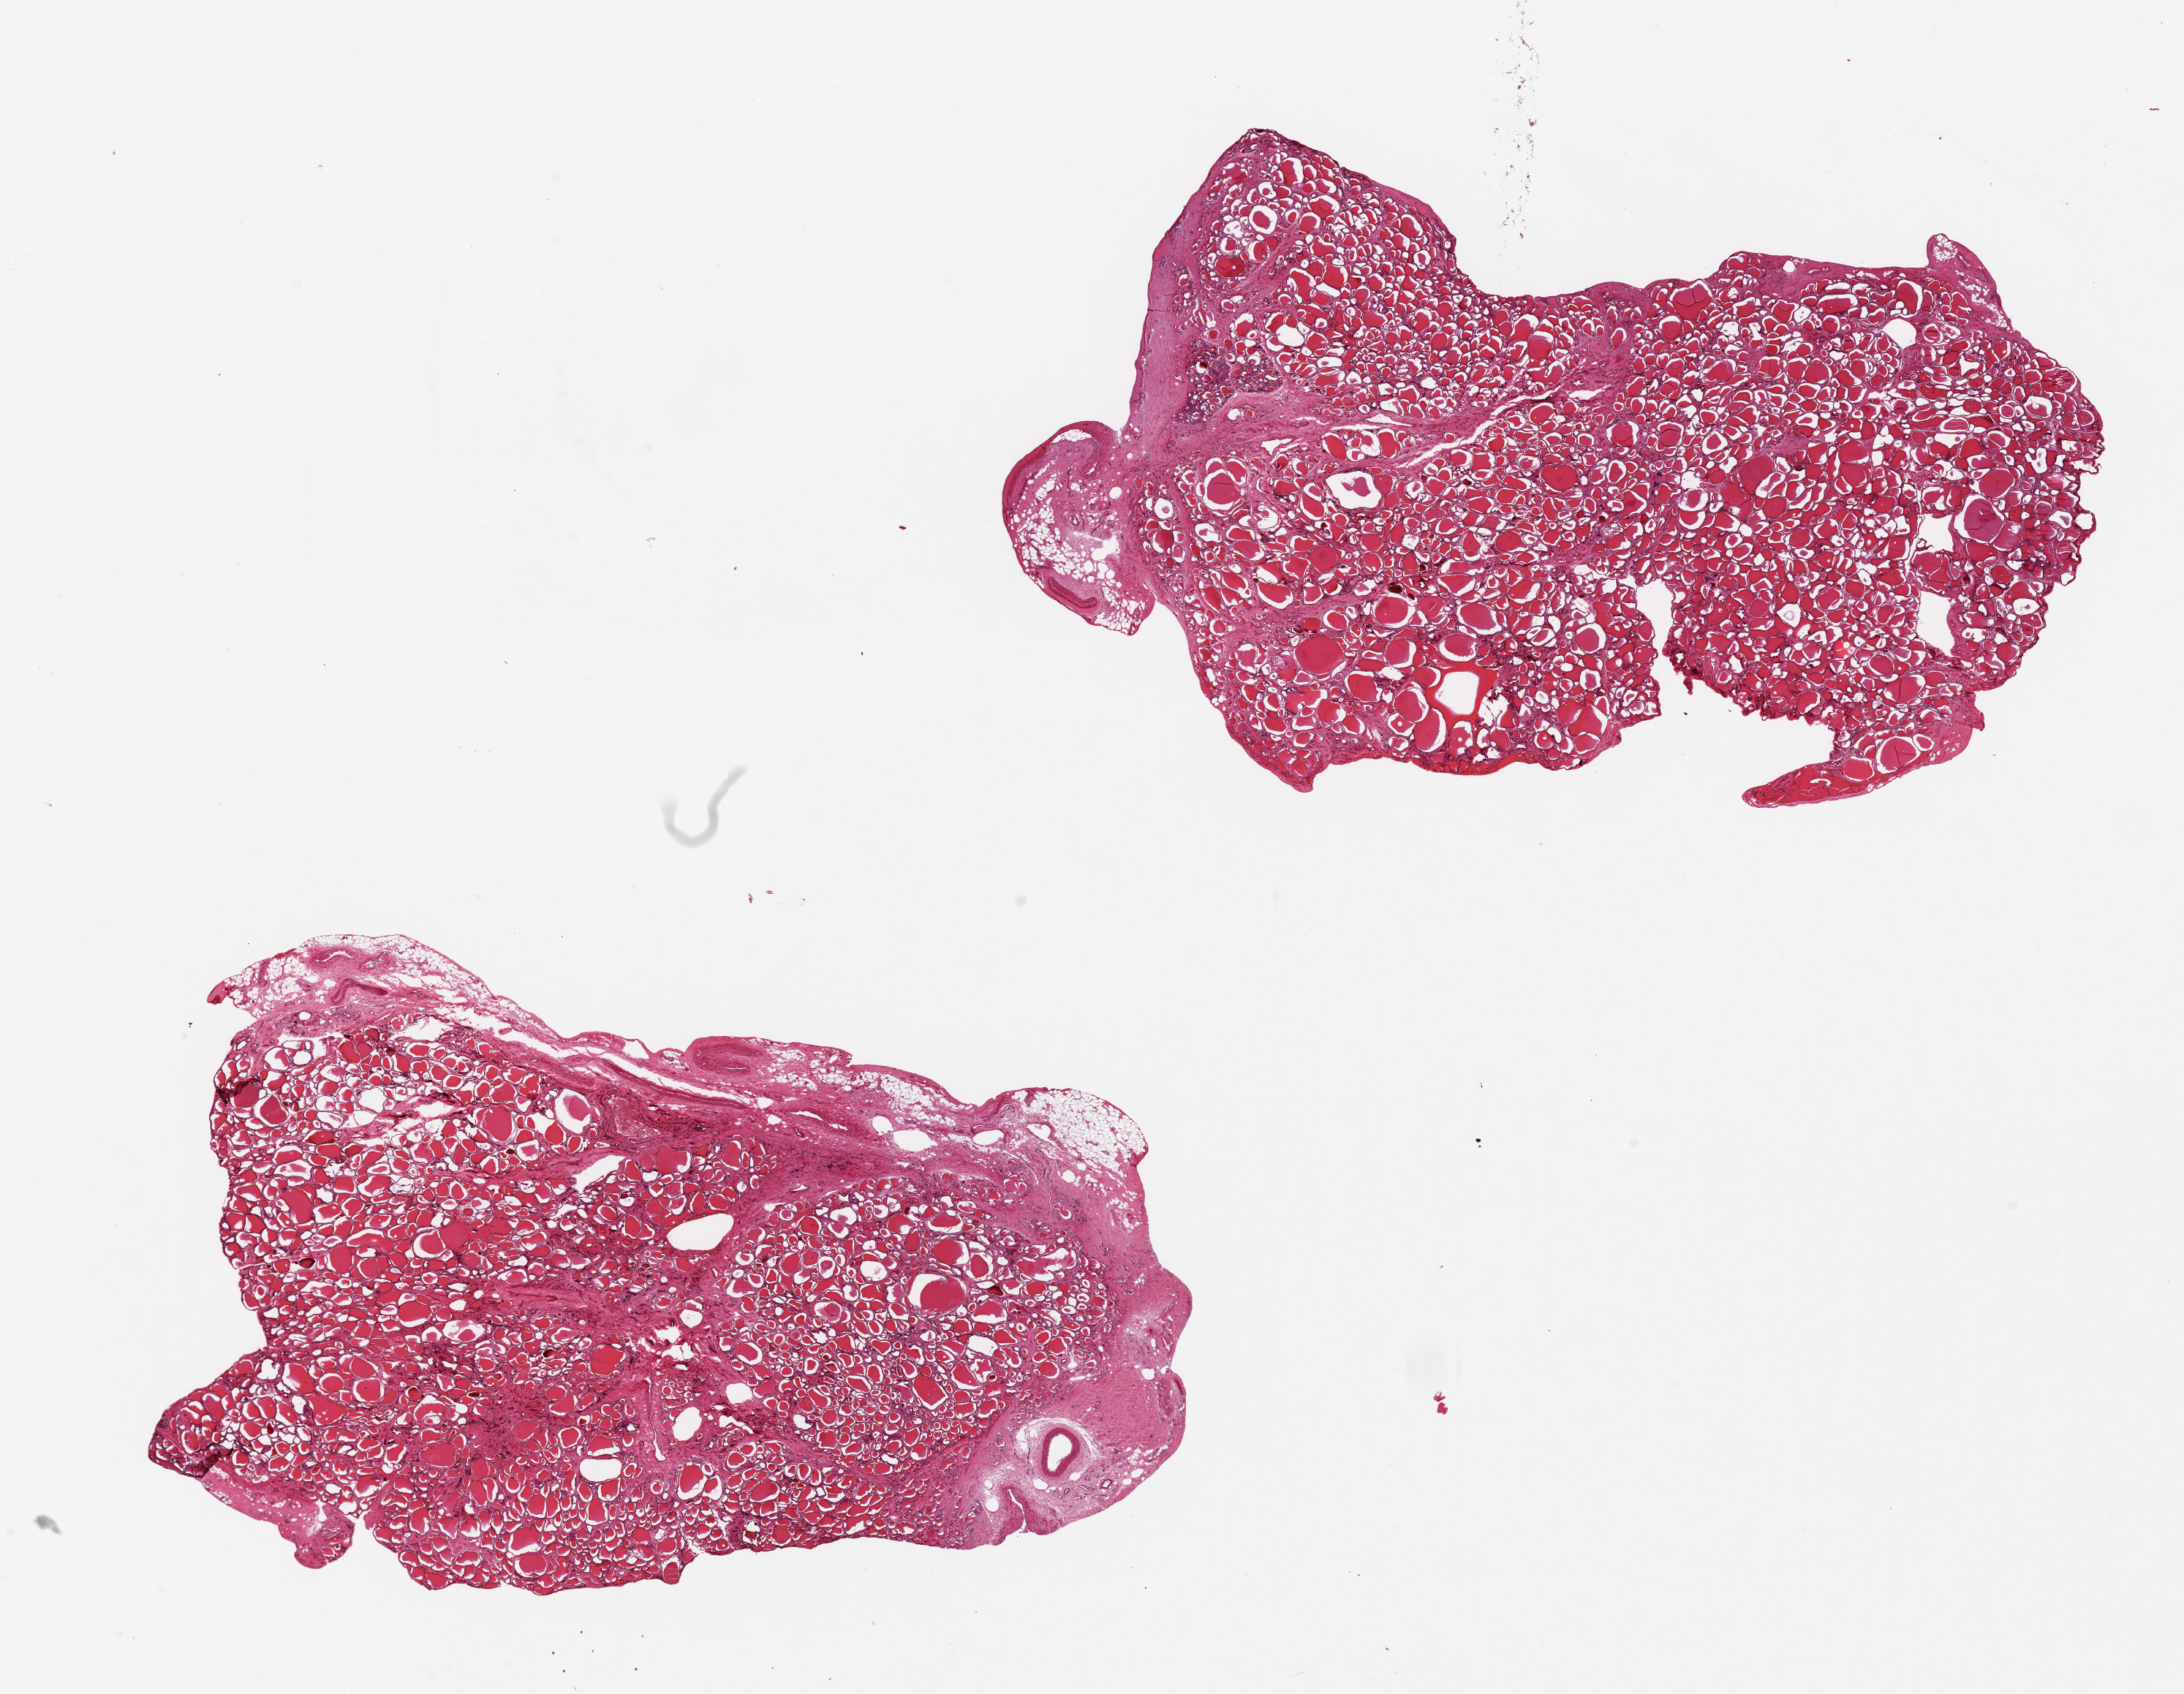
Digitized hematoxylin and eosin (H&E)-stained section, shown as a low-resolution overview of the whole scanned area (about 23.6 x 18.3 mm). PAXgene-fixed, paraffin-embedded tissue. Sampled site (target tissue): thyroid. Donor tissue sample.
• review note (as recorded): 2 pieces 10x6 mm; 10% peripheral fibroadipose